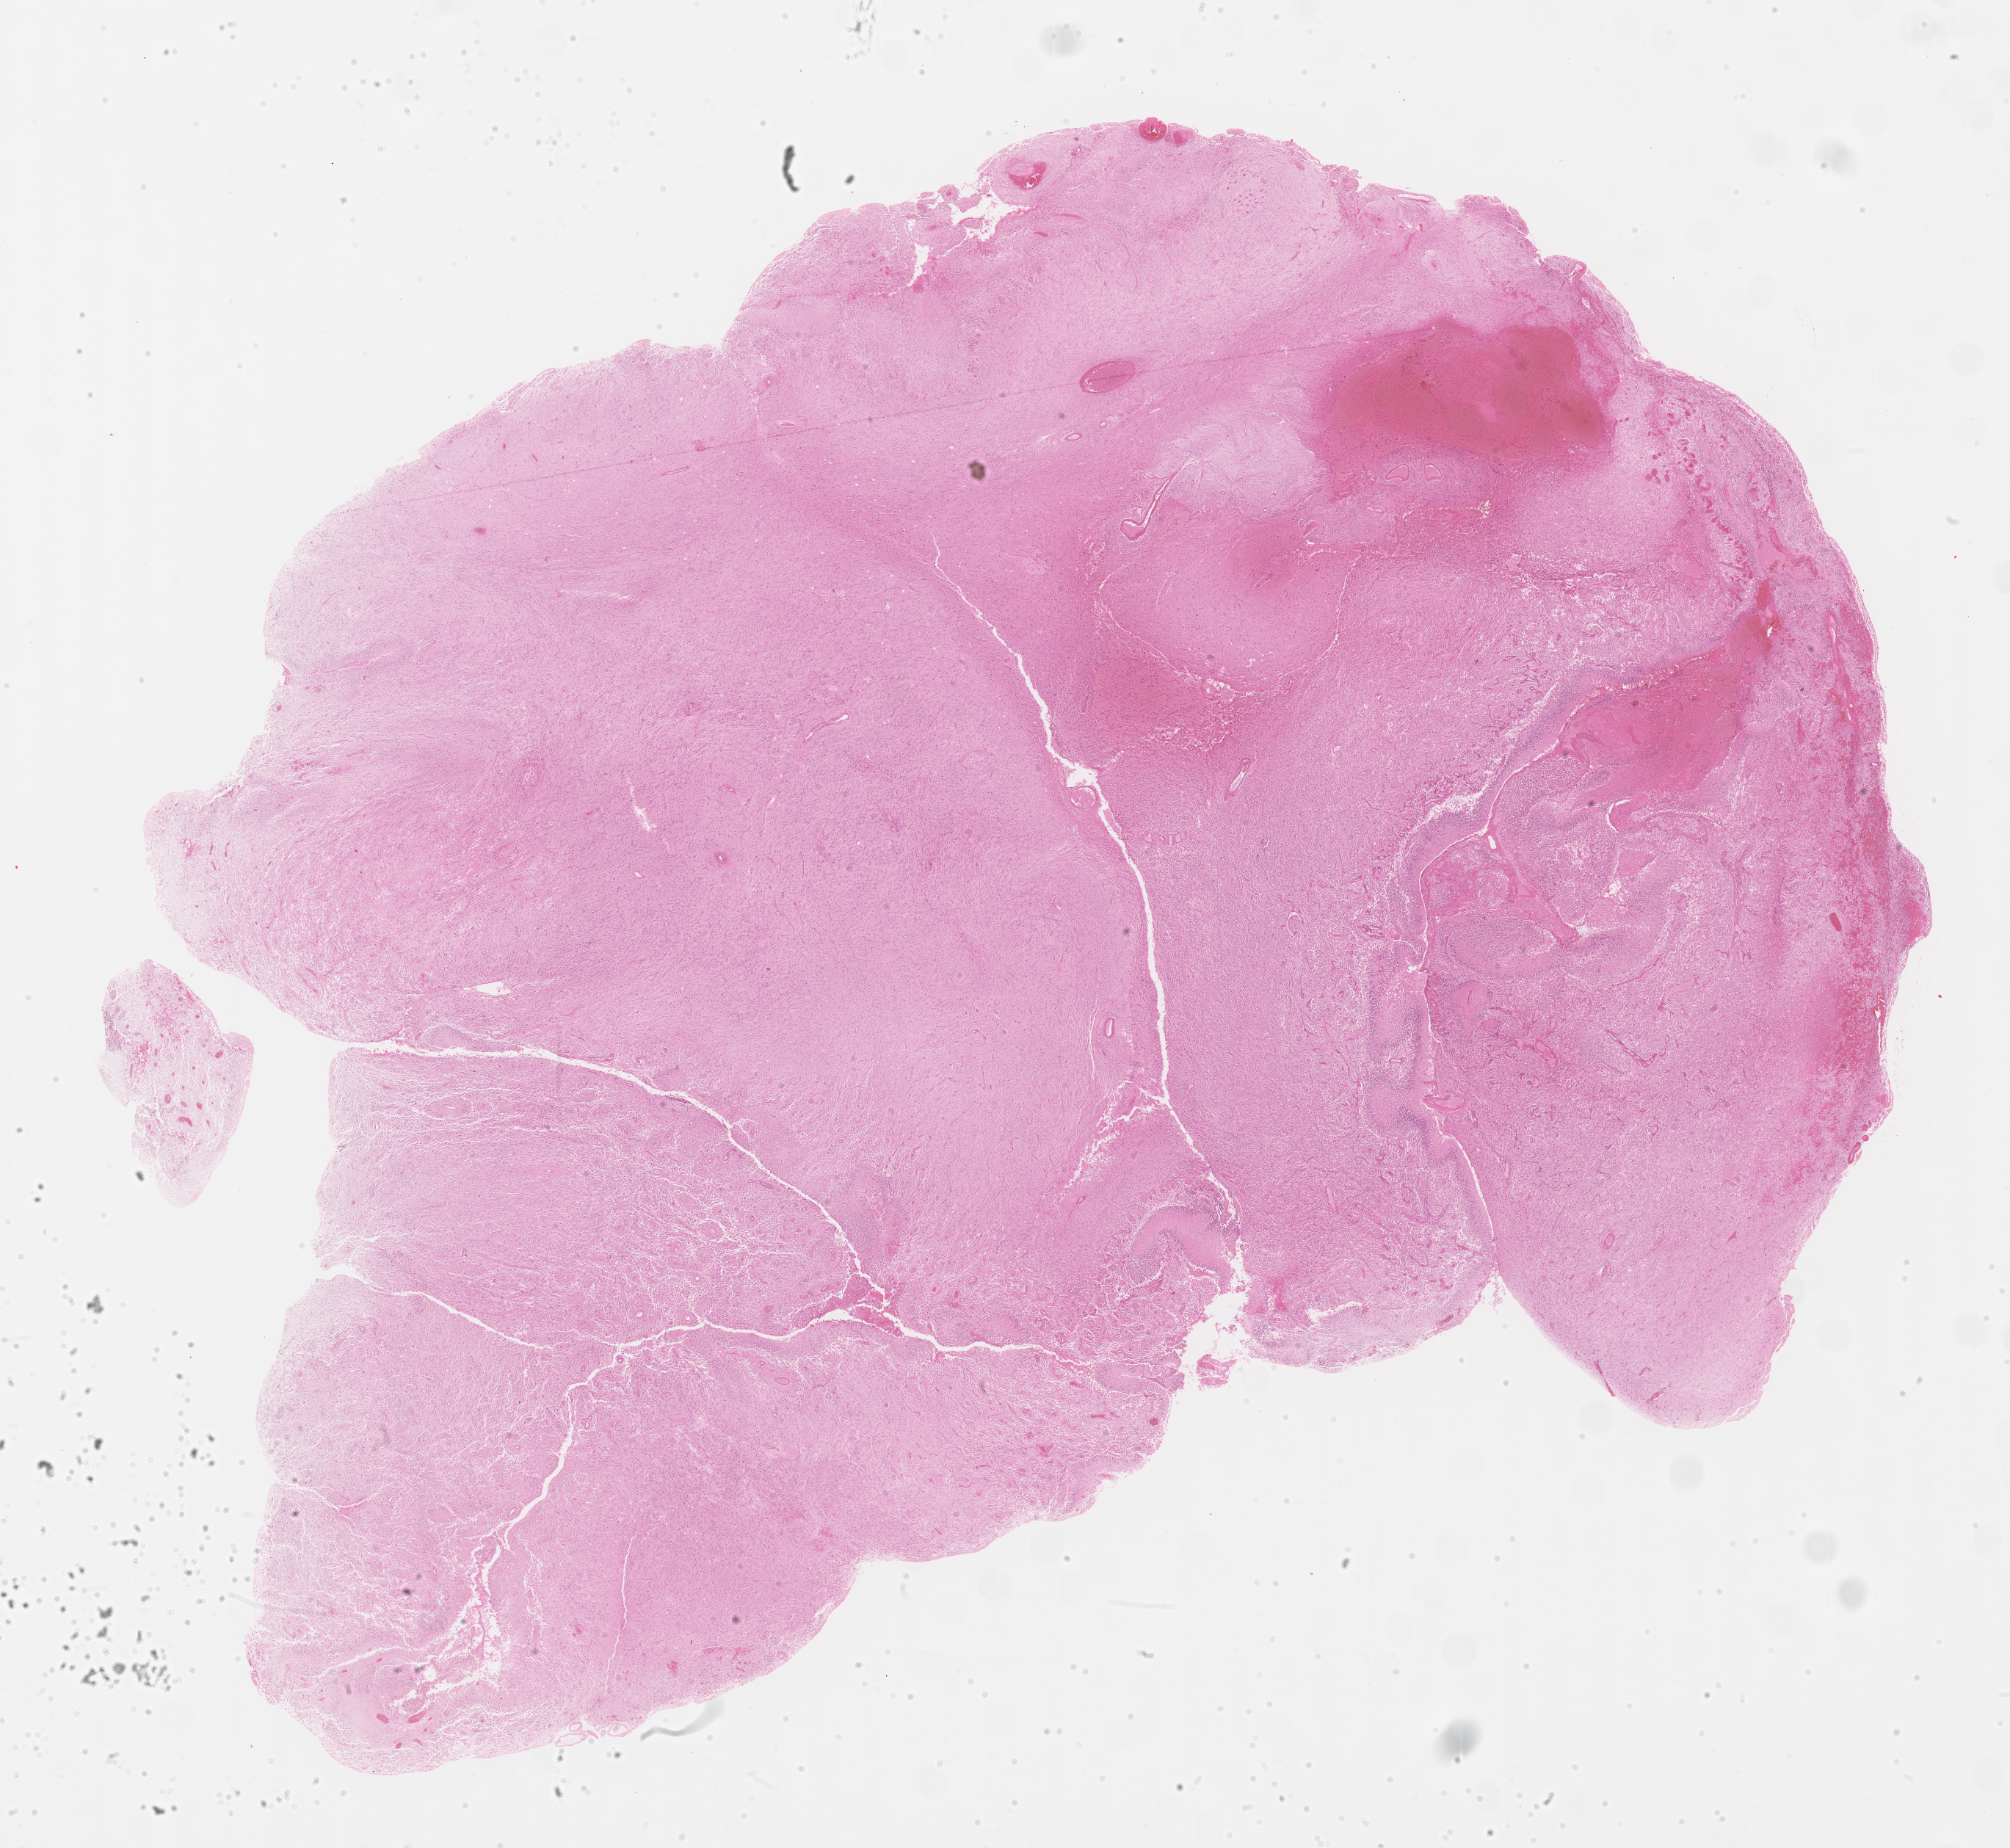
Whole-slide histology image, H&E — whole scanned area (about 22.2 x 20.4 mm, acquisition: 40x scan) shown as a low-resolution overview; formalin-fixed paraffin-embedded (FFPE) diagnostic section; primary tumour sample from the brain. Patient: female, age at initial diagnosis 45 years.
- histologic diagnosis: Glioblastoma